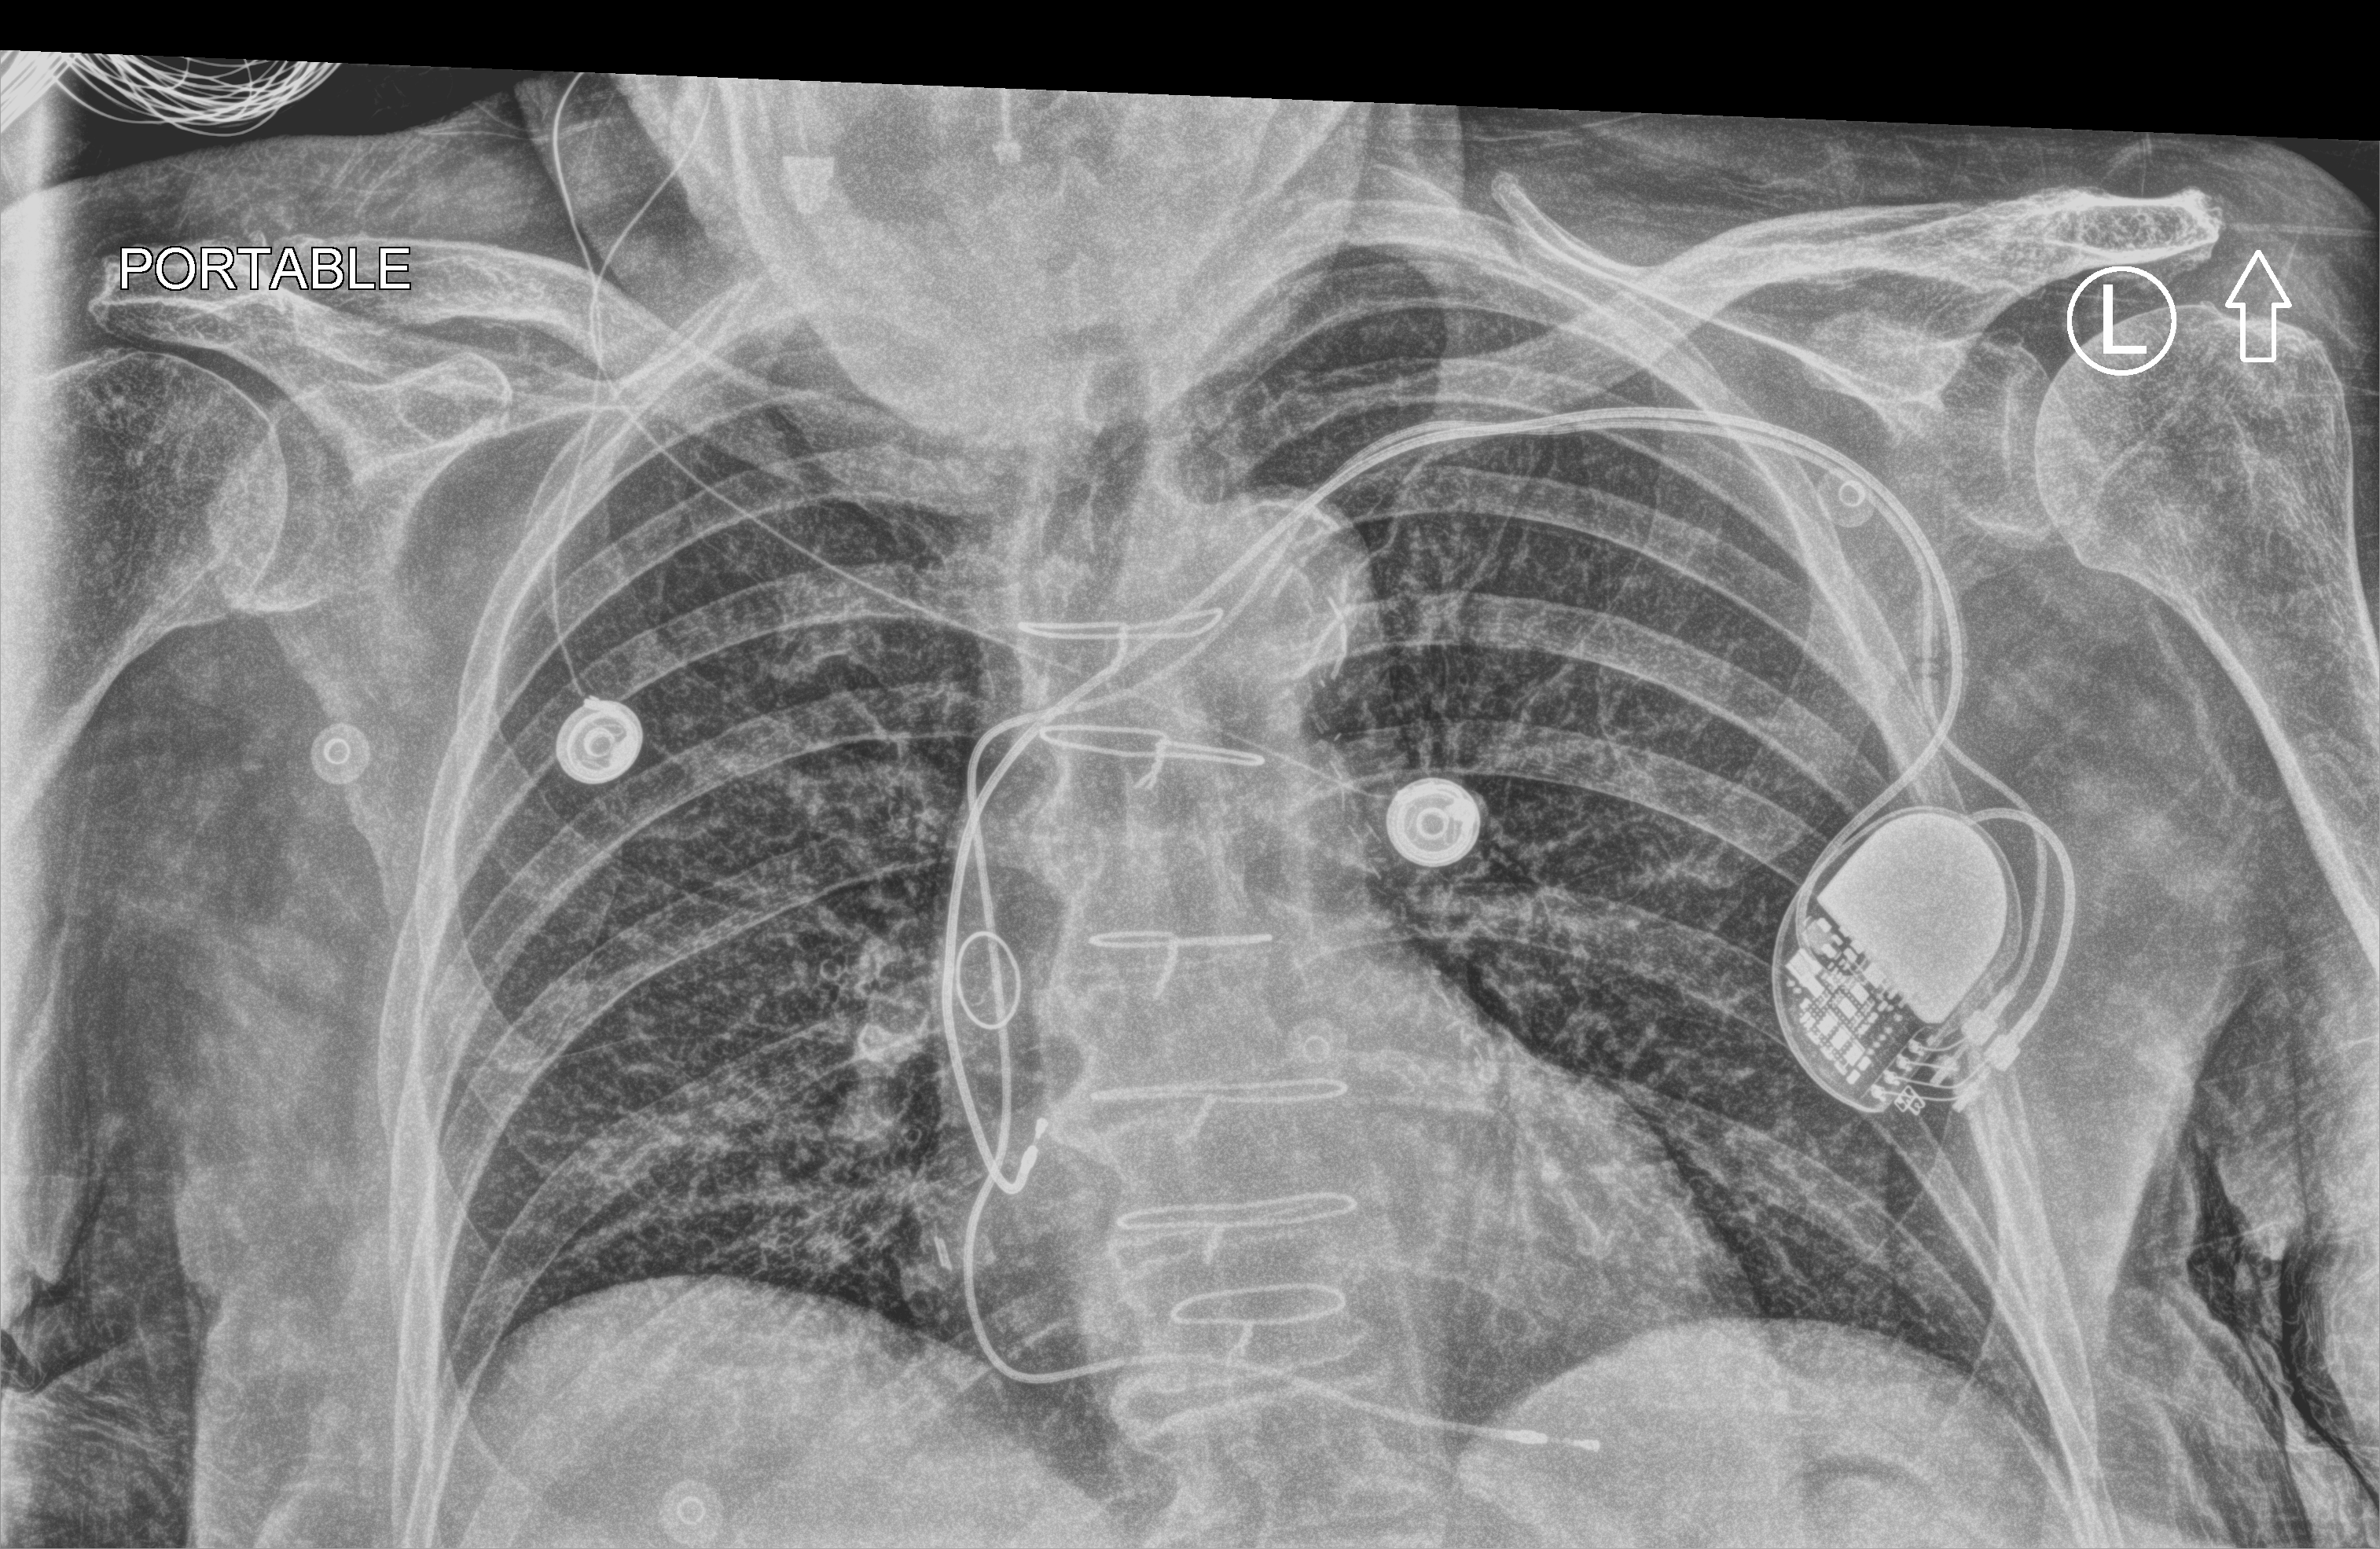
Chest X-ray (portable); anteroposterior (AP) projection. Female patient hospitalised with COVID-19, age 75–90 years.
From the hospital-stay record, not from the radiograph (when in the stay this image was taken is not recorded):
- mechanically ventilated during this hospital stay: no